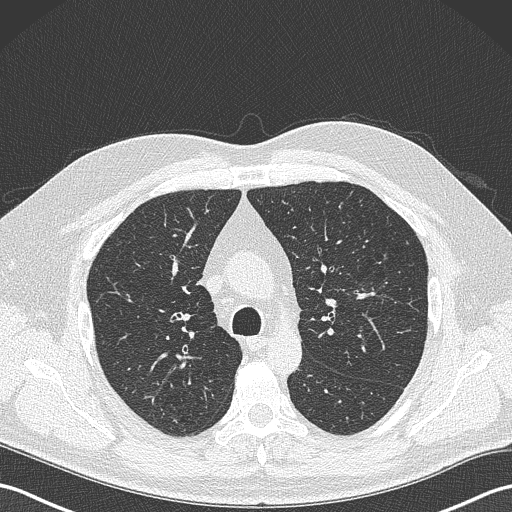
Low-dose screening chest CT, one axial slice; position 238 of 343 along the scan axis; reconstruction kernel B50f; 120 kVp; lung window (W 1500 / L -600 HU); 512 × 512 image matrix, field of view 350 × 350 mm.
Outlined on this slice (manually delineated by an expert):
- lesion 1 (tumor, upper lobe of left lung): box from (x=355, y=287) to (x=375, y=300) px